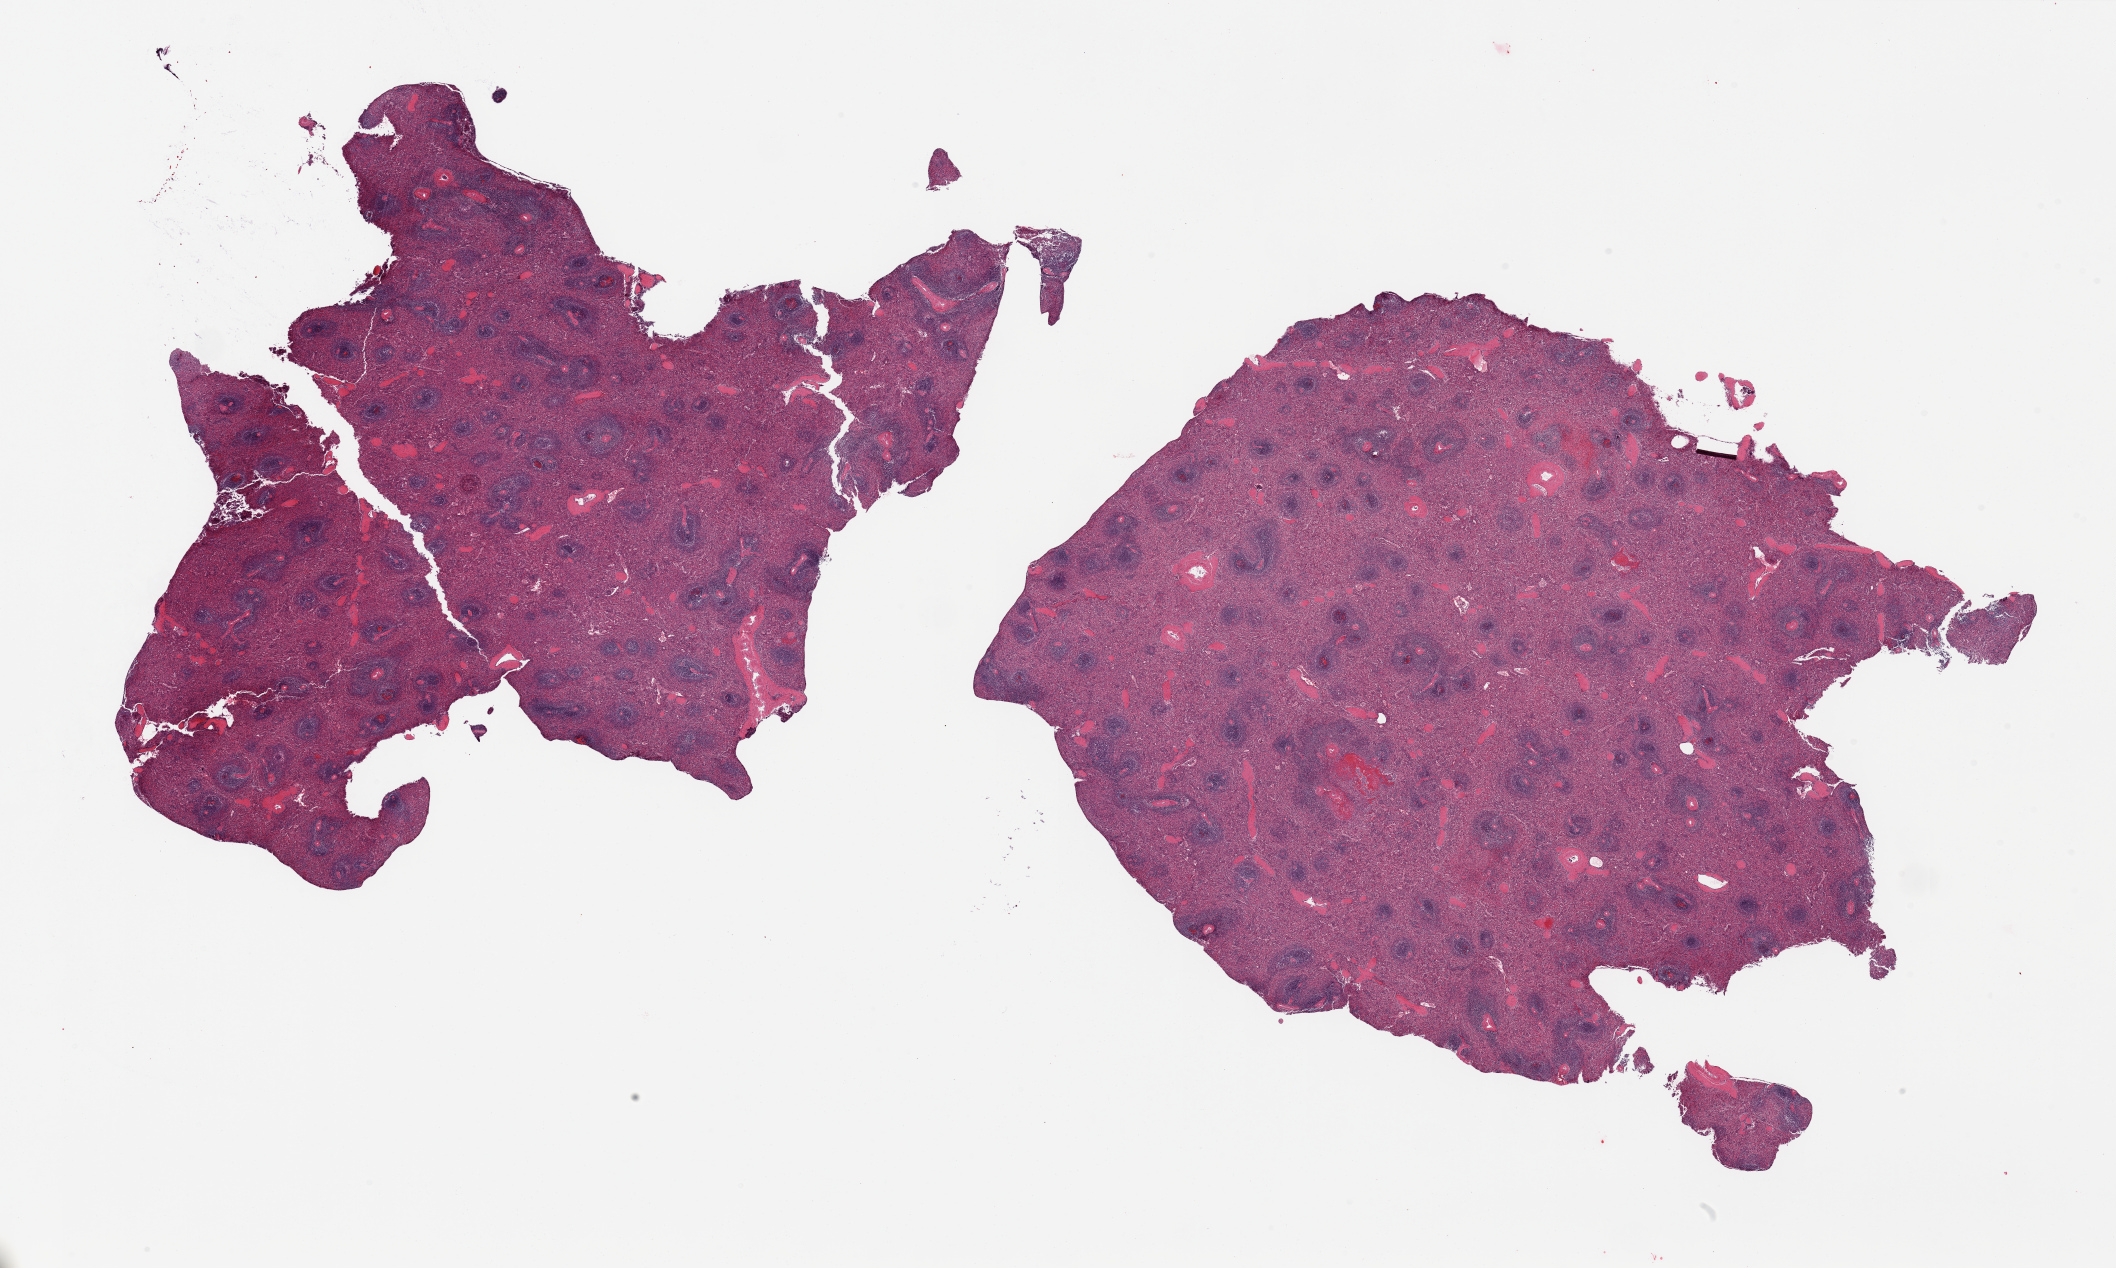
Whole-slide image, hematoxylin and eosin (H&E) stain, brightfield, low-resolution overview of the scanned area, about 33.5 x 20.1 mm (acquisition: 20x scan), PAXgene-fixed, paraffin-embedded tissue, target tissue: spleen, donor tissue sample. Donor sex: male.
• pathologist's review note for this sample: 2 pieces; not congested